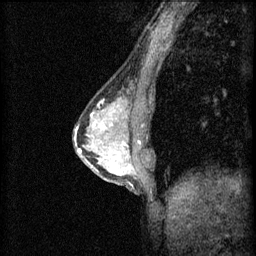
Breast MRI (dynamic contrast-enhanced), one sagittal slice. Position 27 of 60 along the scan axis. 3 images stored at this slice position (order not interpretable as contrast timing). 1.5 T. TE 4.2 ms, TR 8.2 ms. 2 mm slice thickness. 256 × 256 image matrix, field of view 180 × 180 mm. Patient: female, 44 years.
Structures marked on this image (semi-automatically segmented with operator editing):
- analysis volume of interest (the breast-tissue region the enhancement analysis was run in; not a lesion): box from (x=102, y=132) to (x=151, y=181) px
- tumour enhancement mask (voxels above the 70 % enhancement threshold inside the analysis volume of interest): (x=110, y=142)–(x=131, y=175)